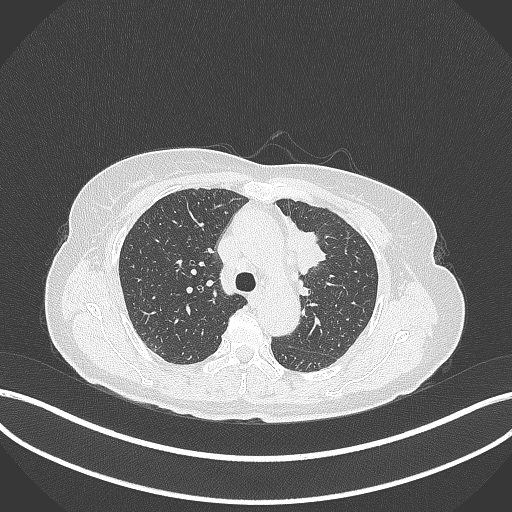
Chest CT, one axial slice. Slice 235 of 369 in the series (ordered by position). Reconstruction kernel B70f. Lung window (W 1500 / L -600 HU). 1 mm slice thickness. 512 × 512 image matrix, field of view 400 × 400 mm. Patient: female, 65 years. Case-level facts recorded for this patient, not image findings: clinical TNM (as recorded): T2a N0 M0.
Structures marked on this image (rectangle marked by the reading radiologist):
- lung tumour (recorded histology: adenocarcinoma): bounding box [x1, y1, x2, y2] px = [281, 215, 330, 277]